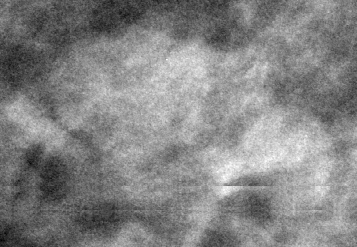
Crop from a digitized film mammogram around one marked abnormality, right breast, MLO view, BI-RADS breast density category 1 (scale 1–4).
- Finding: mass, shape lobulated, margins circumscribed; BI-RADS assessment category 3; subtlety rating 4 on a 1 (subtle) to 5 (obvious) scale; benign without callback (not worked up further).